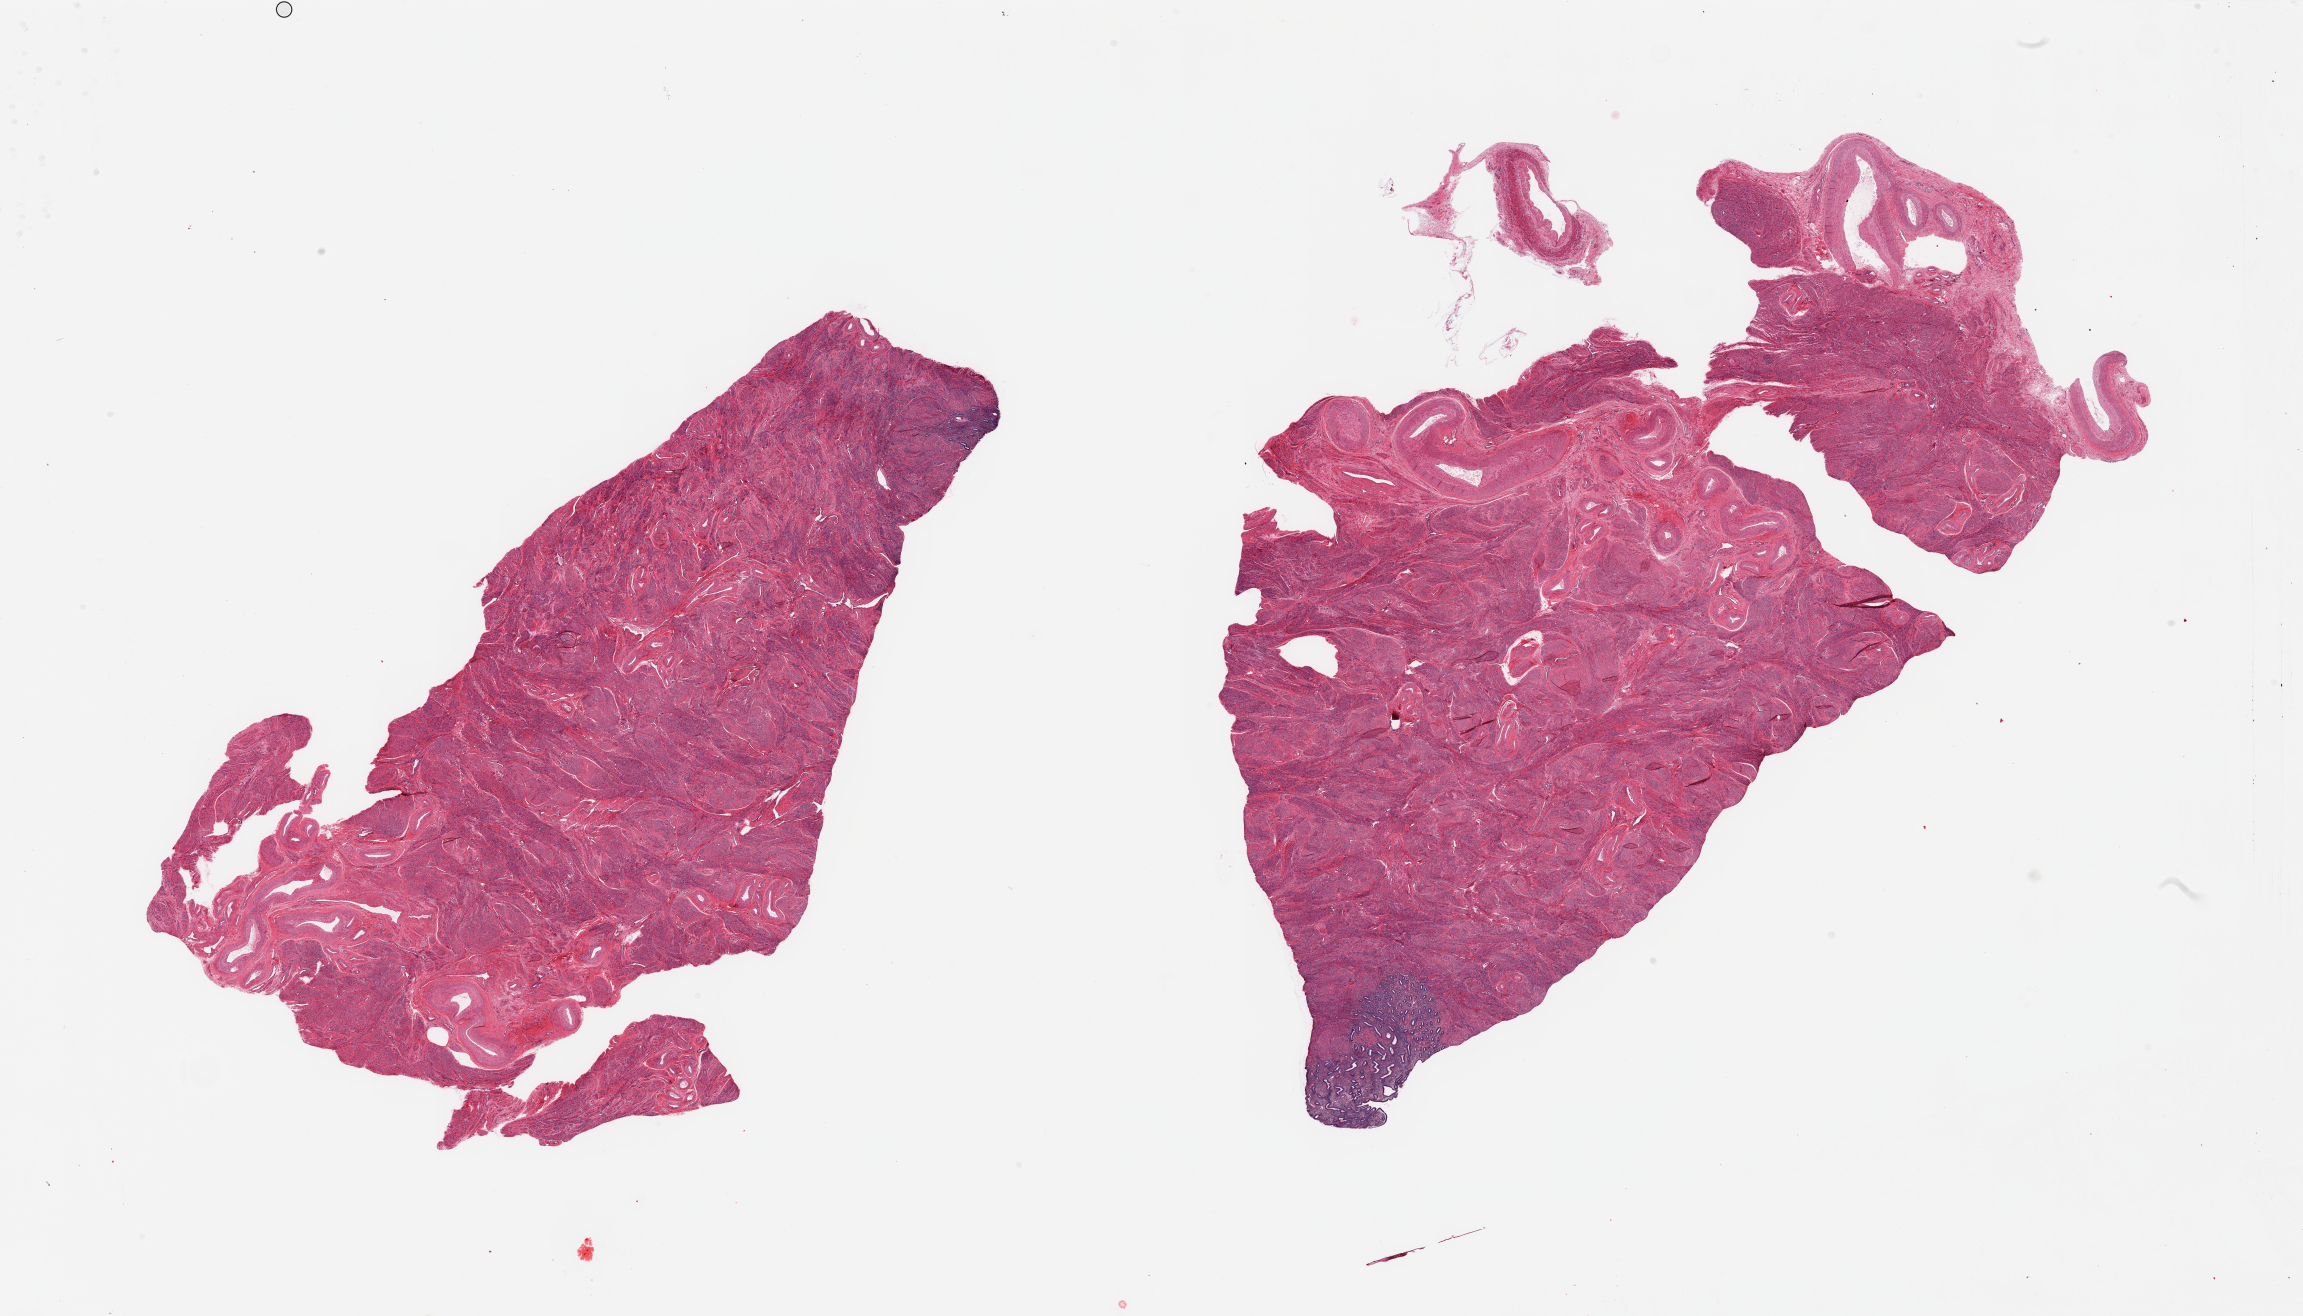
Hematoxylin and eosin (H&E) whole-slide image — low-resolution overview of the scanned area, about 36.4 x 20.8 mm (acquisition: 20x scan). PAXgene-fixed, paraffin-embedded tissue. Sampled site (target tissue): uterus. Tissue donor sample. Donor: female.
- review note (as recorded): 2 pieces, mainly myometrium; 2.5mm focus well fixed endometrium